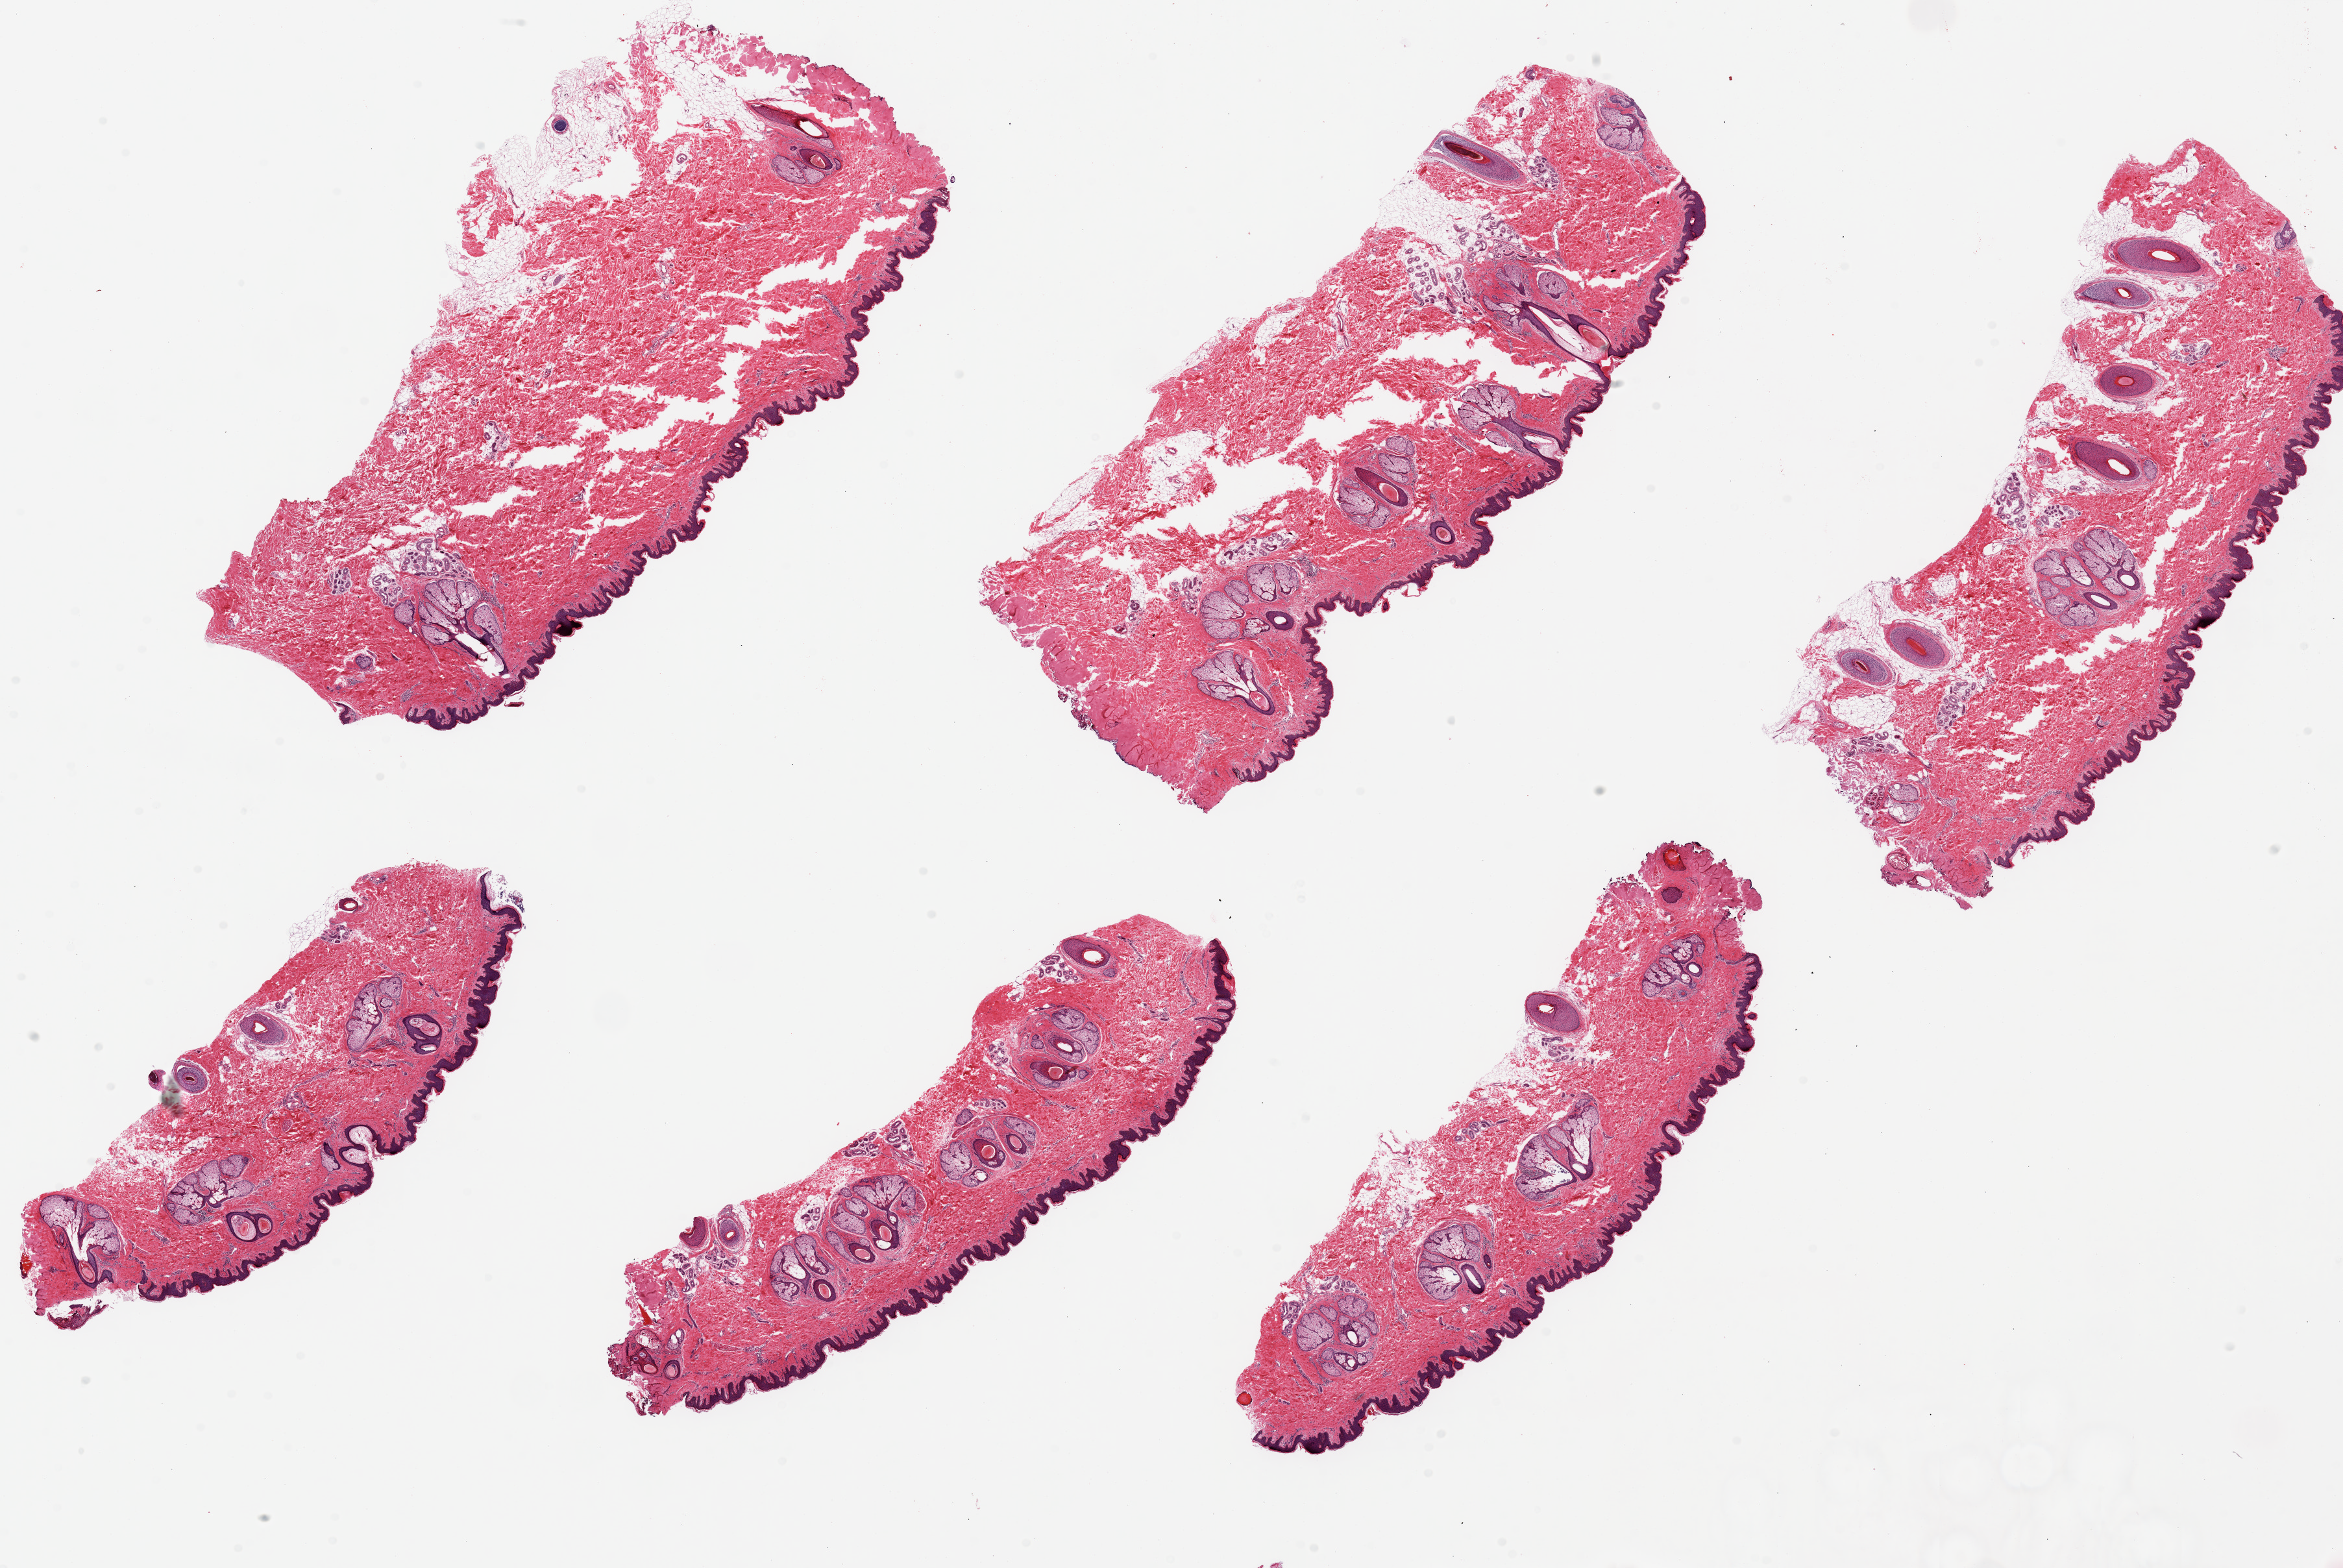
H&E whole-slide image, a low-resolution overview of the entire scanned area, about 28.5 x 19.1 mm; PAXgene-fixed paraffin-embedded (PFPE) section; sampled site (target tissue): skin of suprapubic region; donor tissue sample. Male donor.
* review note (as recorded): 6 pieces ~9x3mm; Squamous epithelium is ~2-3% thickness, prominent sebaceous glands noted